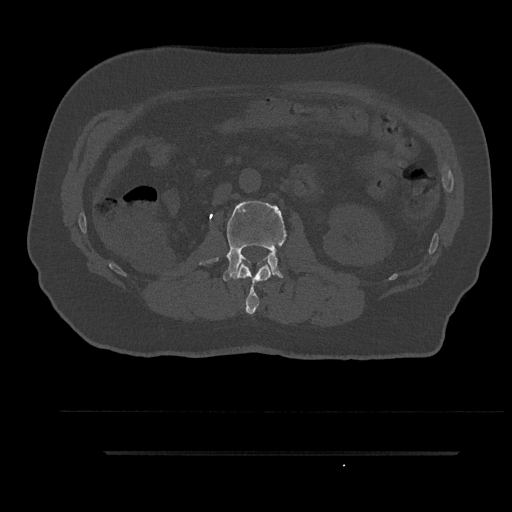
CT including the spine, one axial slice; position 131 of 797 along the scan axis; reconstruction kernel Br40s/3; 120 kVp; bone window (W 1800 / L 400 HU); 0.5 mm slice thickness; 512 × 512 image matrix. Male patient, age 63 years. Case-level facts recorded for this patient, not image findings: primary cancer: renal.
Structures marked on this image (semi-automatic segmentation, software-assisted and operator-edited):
- L1 vertebra: bounding box (x1, y1, x2, y2) in pixels: (234, 262, 272, 314)
- L2 vertebra: (200, 201, 287, 281)